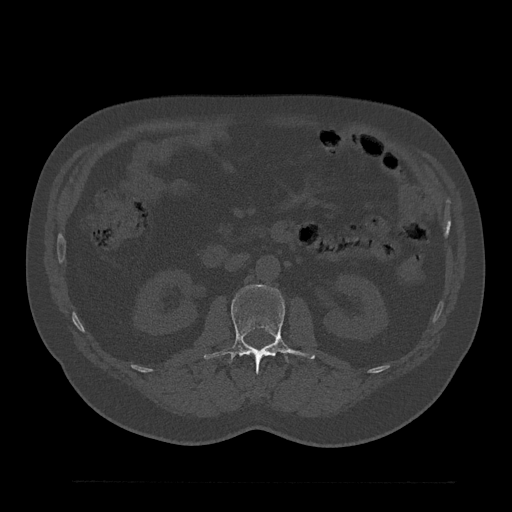
CT including the spine, one axial slice. Slice 101 of 797 in the series (ordered by position). 120 kVp. Bone window (W 1800 / L 400 HU). 512 × 512 image matrix. Patient: male, 61 years. Case-level facts recorded for this patient, not image findings: primary cancer: prostate.
Structures marked on this image (semi-automatically segmented with operator editing):
- L1 vertebra: bounding box <263,354,267,355> (left, top, right, bottom; pixels)
- L2 vertebra: <204,285,316,371>